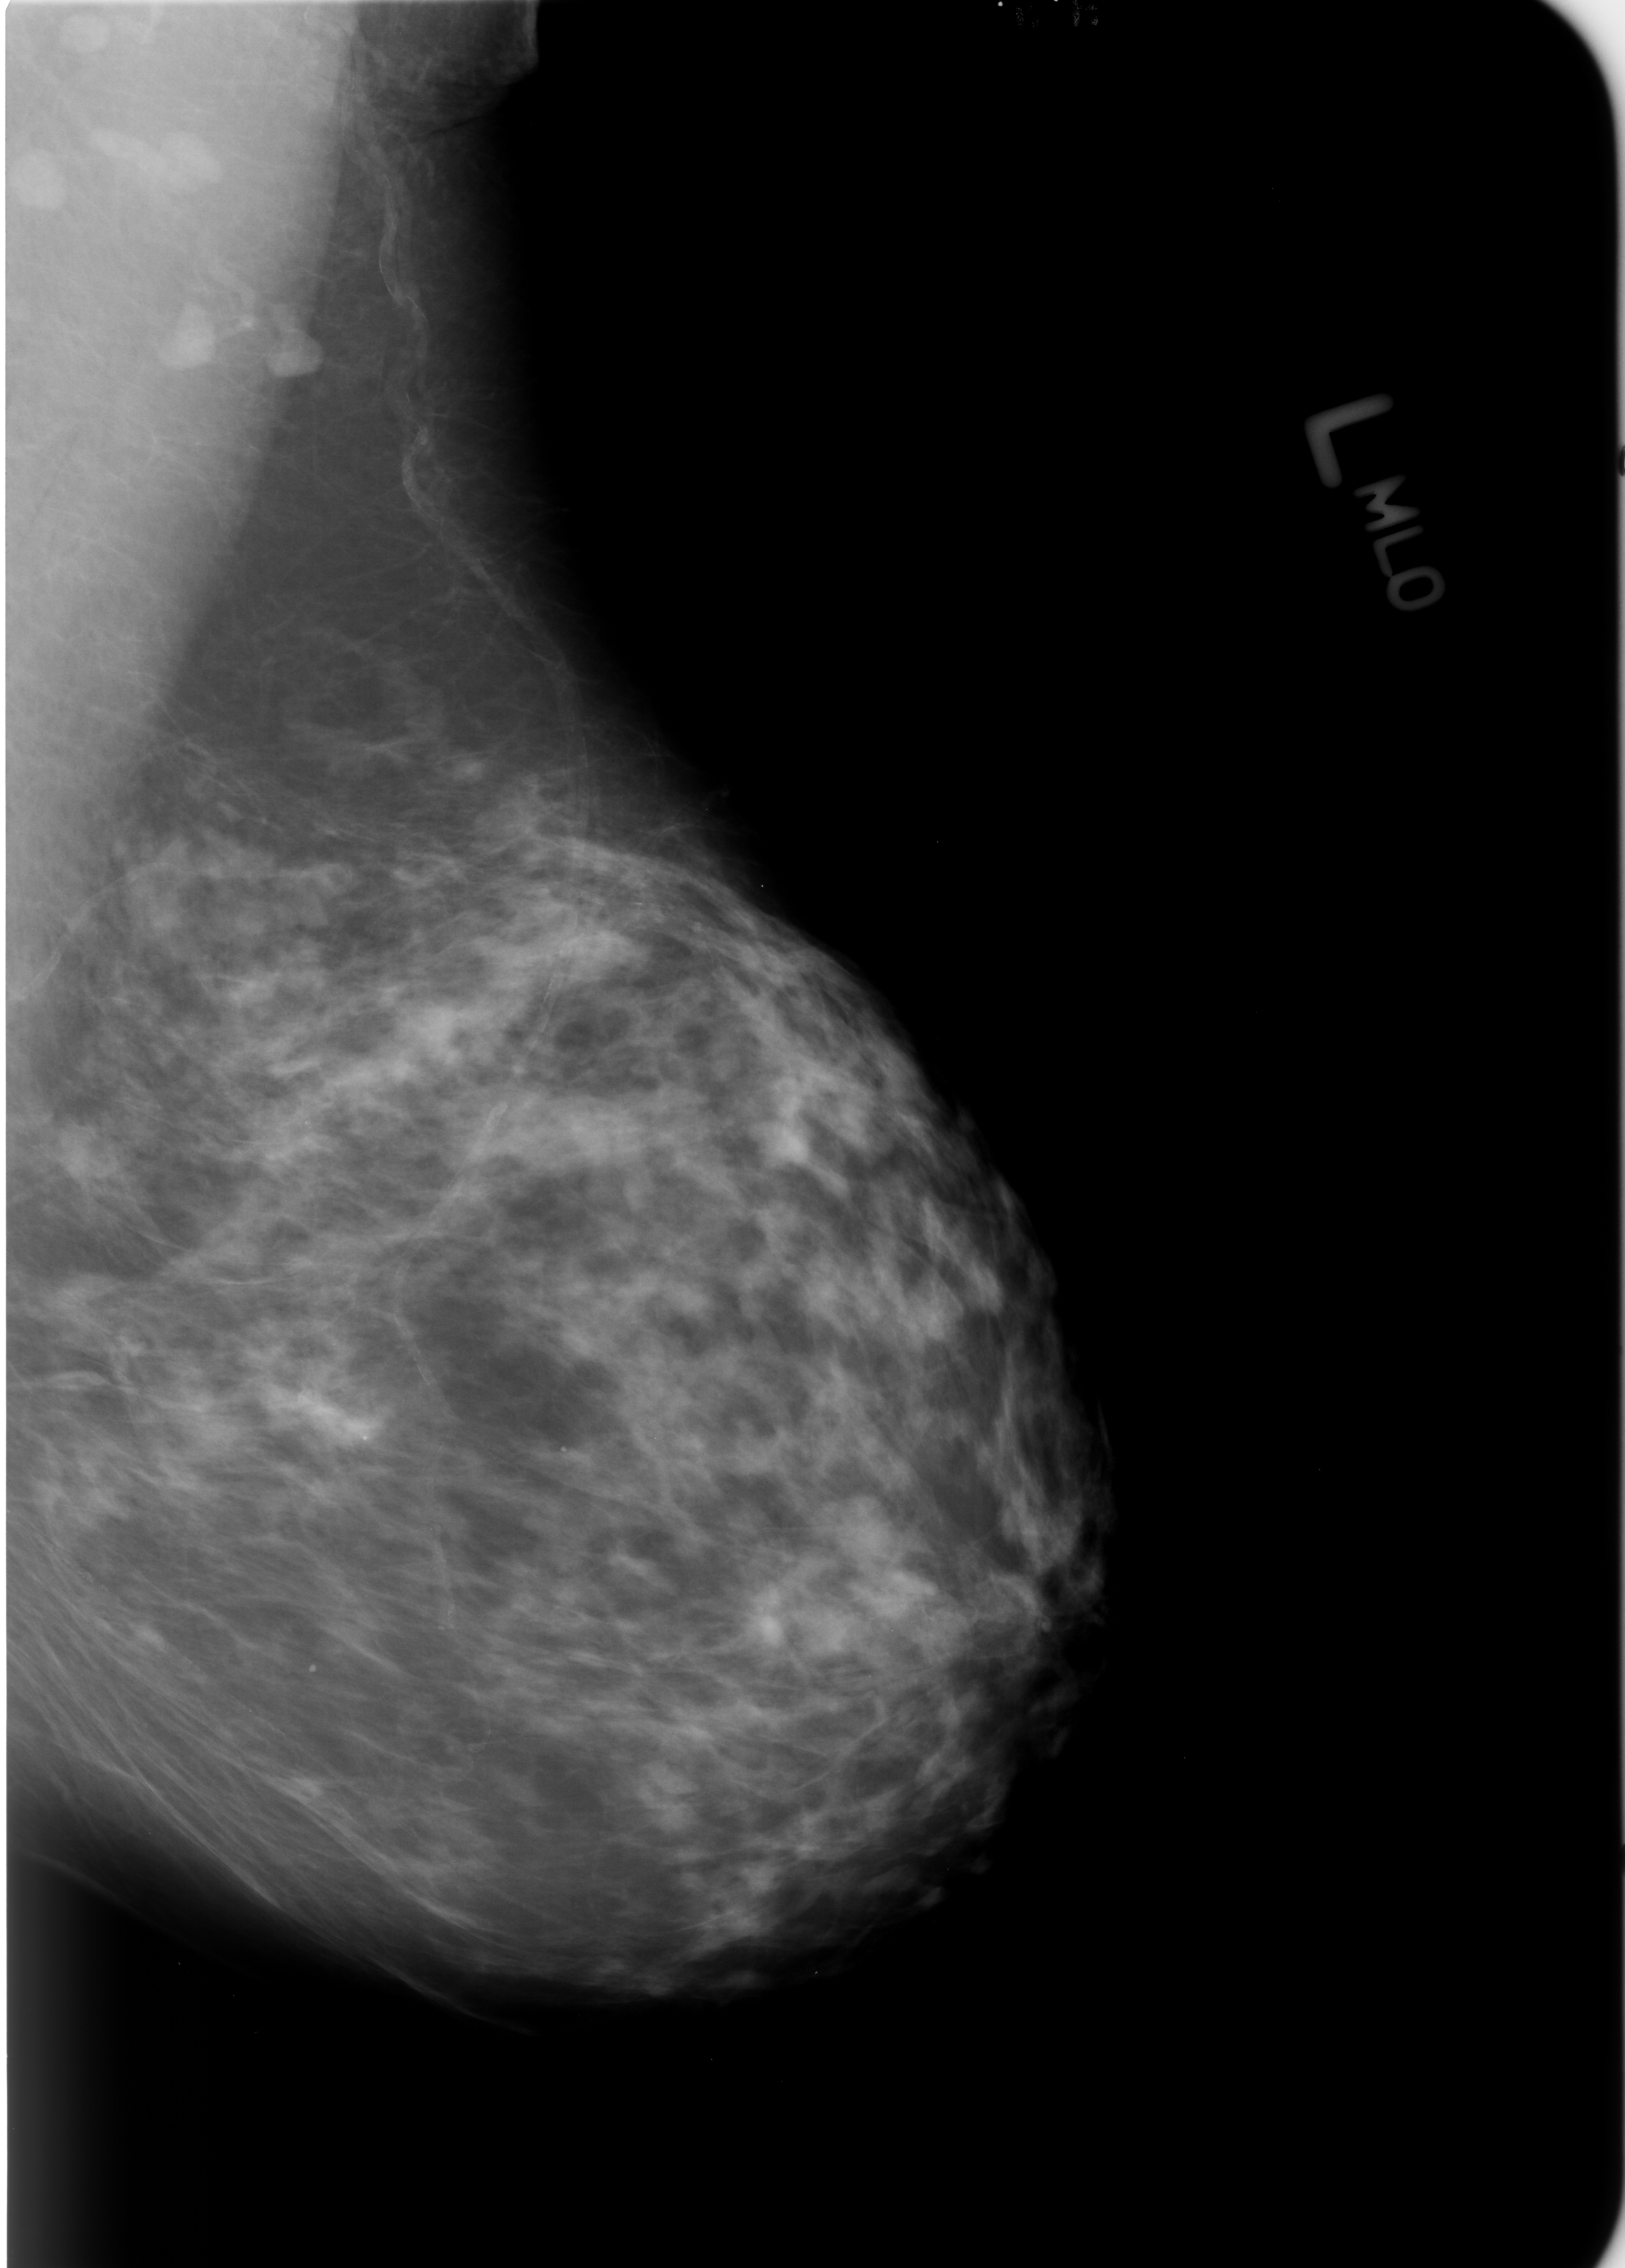
Scanned film-screen mammogram; left breast; mediolateral oblique (MLO) view; BI-RADS breast density category 2 (scale 1–4); 1625 × 2268 image matrix.
Marked abnormalities (boxes around the expert regions of interest):
- Finding 1 of 4: calcifications, morphology punctate; BI-RADS assessment category 2; outcome (as recorded, no biopsy): benign without callback (not worked up further): bounding box <284,1641,350,1712> (left, top, right, bottom; pixels)
- Finding 2 of 4: calcifications, morphology punctate; BI-RADS assessment category 2; subtlety rating 4 on a 1 (subtle) to 5 (obvious) scale; benign; no additional work-up was recommended (outcome (as recorded, no biopsy): benign without callback): <335,1413,410,1476>
- Finding 3 of 4: calcifications, morphology vascular; BI-RADS assessment category 2; subtlety rating 4 on a 1 (subtle) to 5 (obvious) scale; outcome (as recorded, no biopsy): benign without callback (not worked up further): <383,399,599,1664>
- Finding 4 of 4: calcifications, morphology punctate; BI-RADS assessment category 2; benign; no additional work-up was recommended (outcome (as recorded, no biopsy): benign without callback): <531,1426,602,1485>